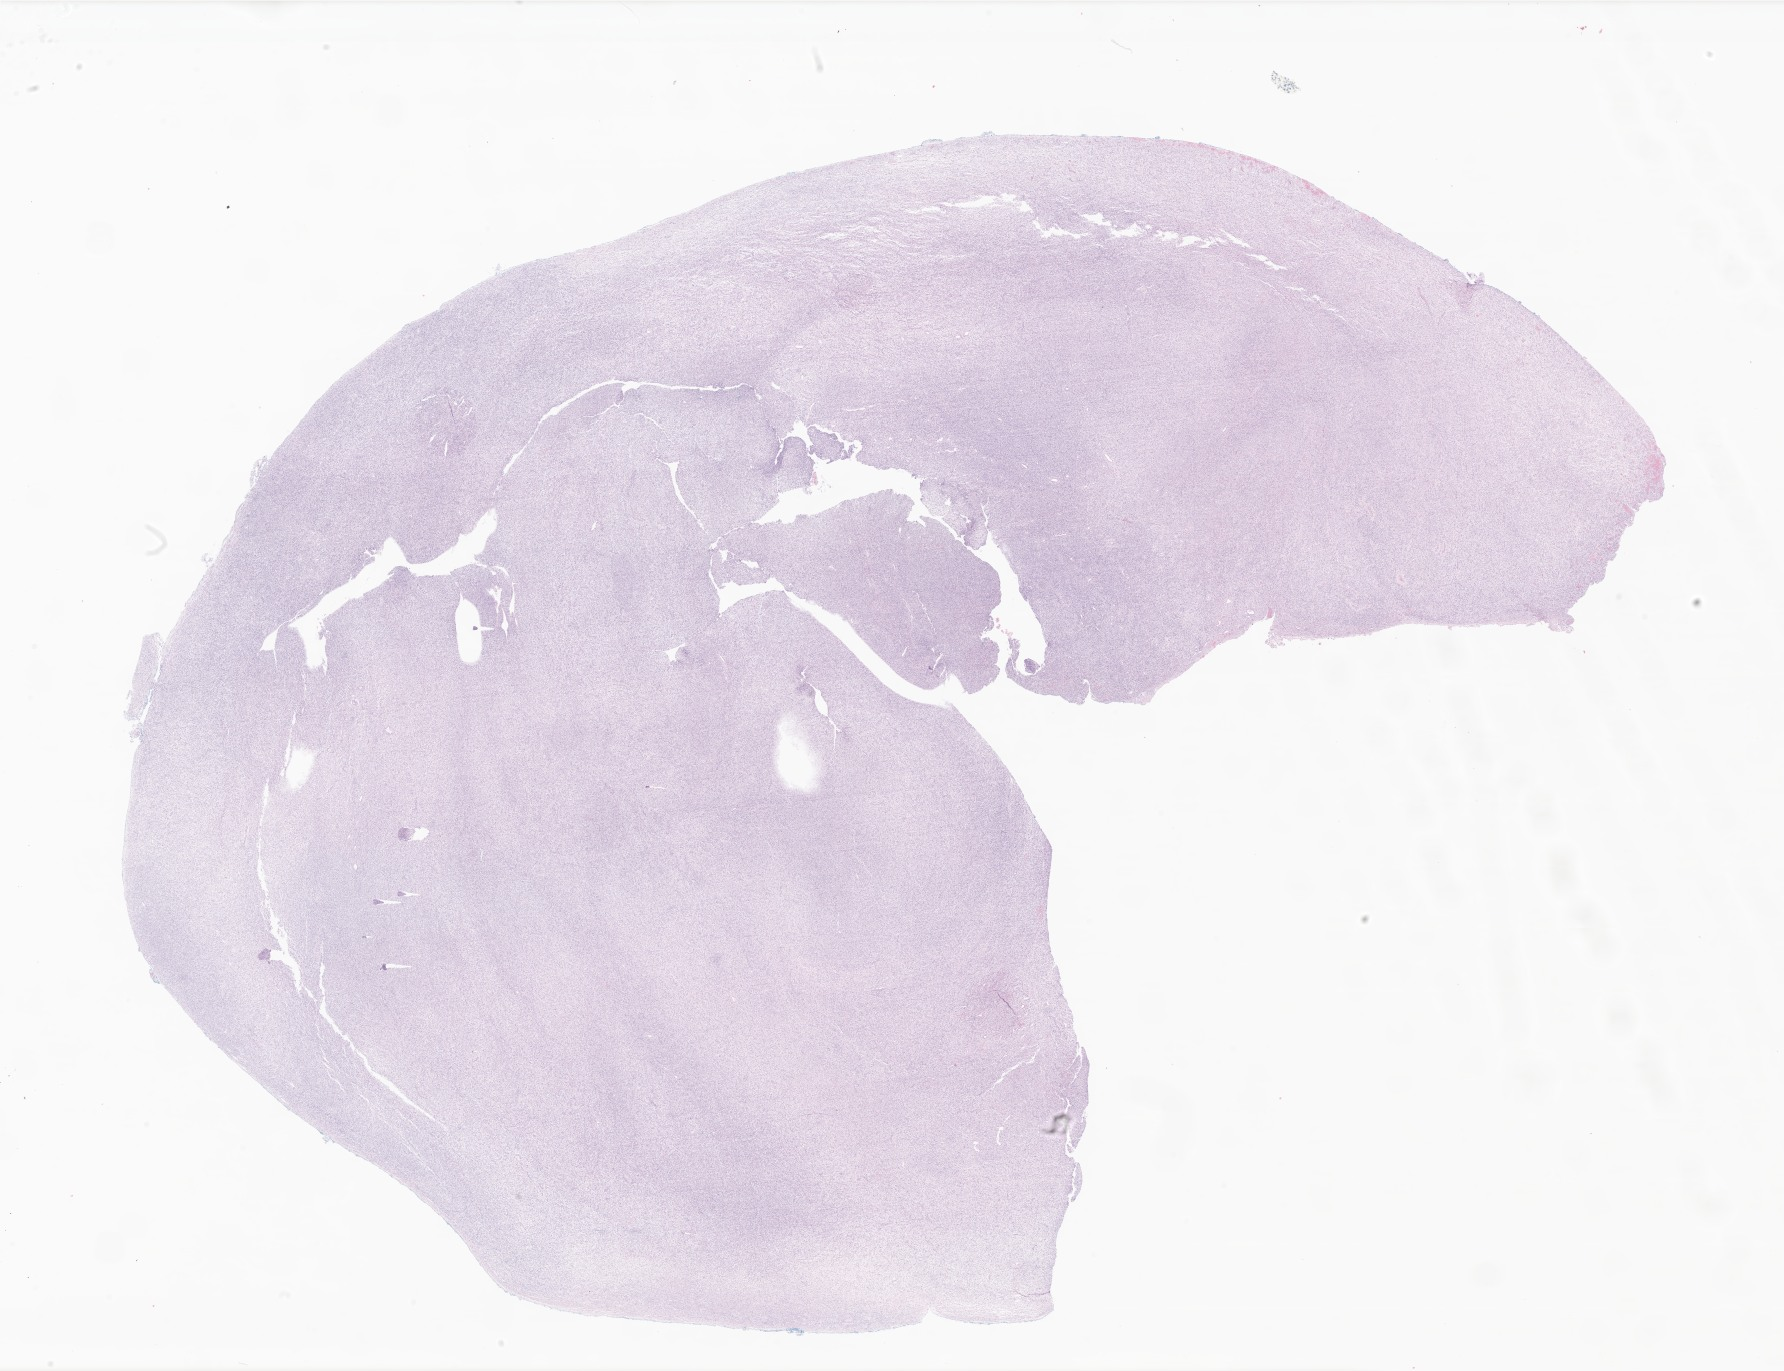
Hematoxylin and eosin (H&E) whole-slide image of tumor tissue from the soft tissues of head and neck — a low-resolution overview of the entire scanned area, about 30.1 x 23.1 mm. Formalin-fixed paraffin-embedded section. Male patient, age 22 days.
Recorded diagnosis: Undifferentiated sarcoma.